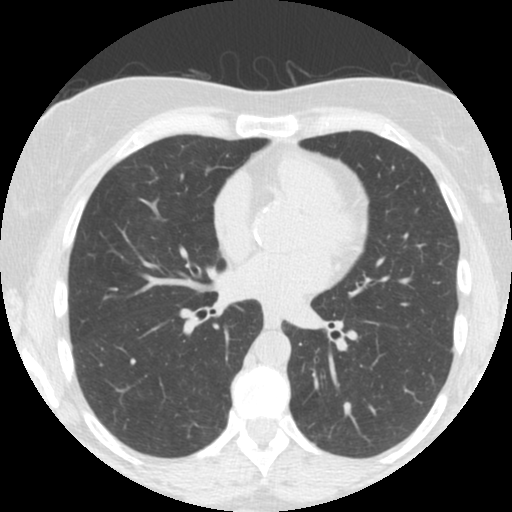
Low-dose screening chest CT, one axial slice. Position 76 of 150 along the scan axis. Reconstruction kernel STANDARD. 120 kVp. Lung window (W 1500 / L -600 HU). 512 × 512 image matrix, field of view 300 × 300 mm.
Annotated regions visible in this slice (manually delineated by an expert):
- lesion 1 (tumor, lower lobe of left lung): bounding box (x1, y1, x2, y2) in pixels: (343, 402, 351, 416)